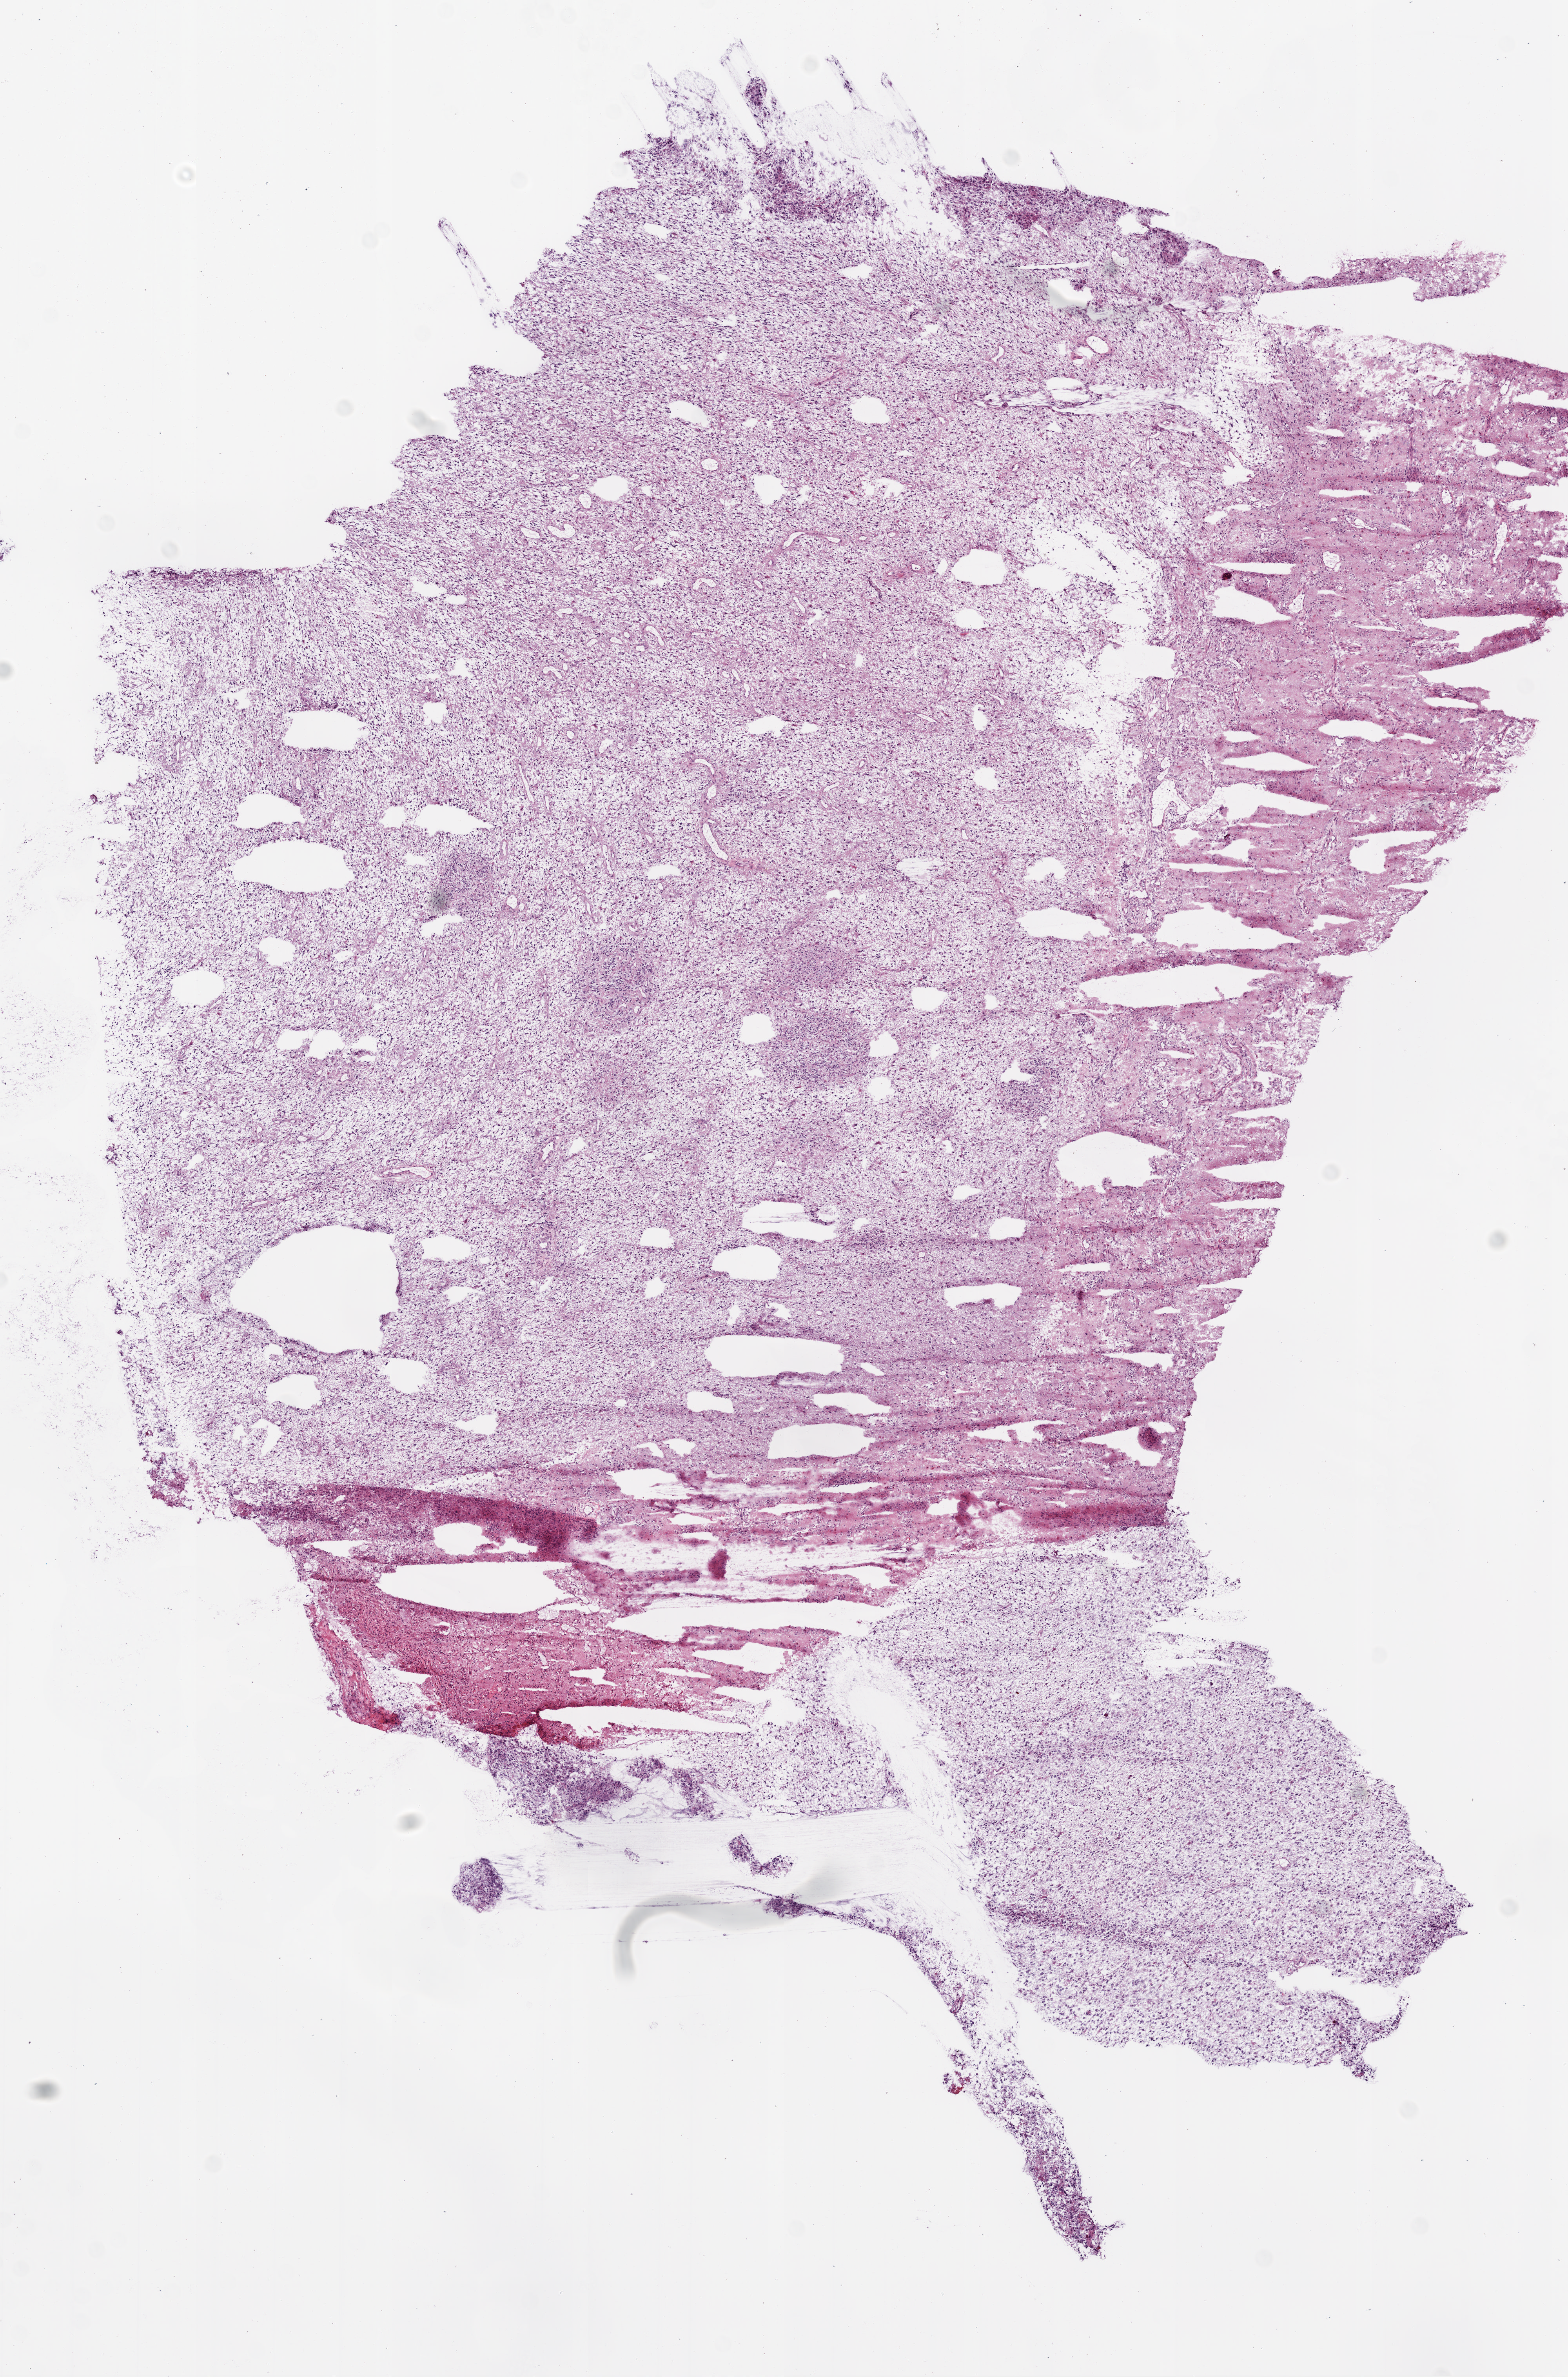
Whole-slide histology image, H&E, low-resolution overview of the scanned area, about 8.0 x 12.2 mm; frozen section; sample: primary tumour, brain. Female, age 28 years at initial diagnosis. Pathologist review of this section (percent, as recorded): tumour cells 80%, tumour nuclei 90%, normal cells 10%, stromal cells 10%, necrosis 0%.
Pathologic diagnosis: Glioblastoma.